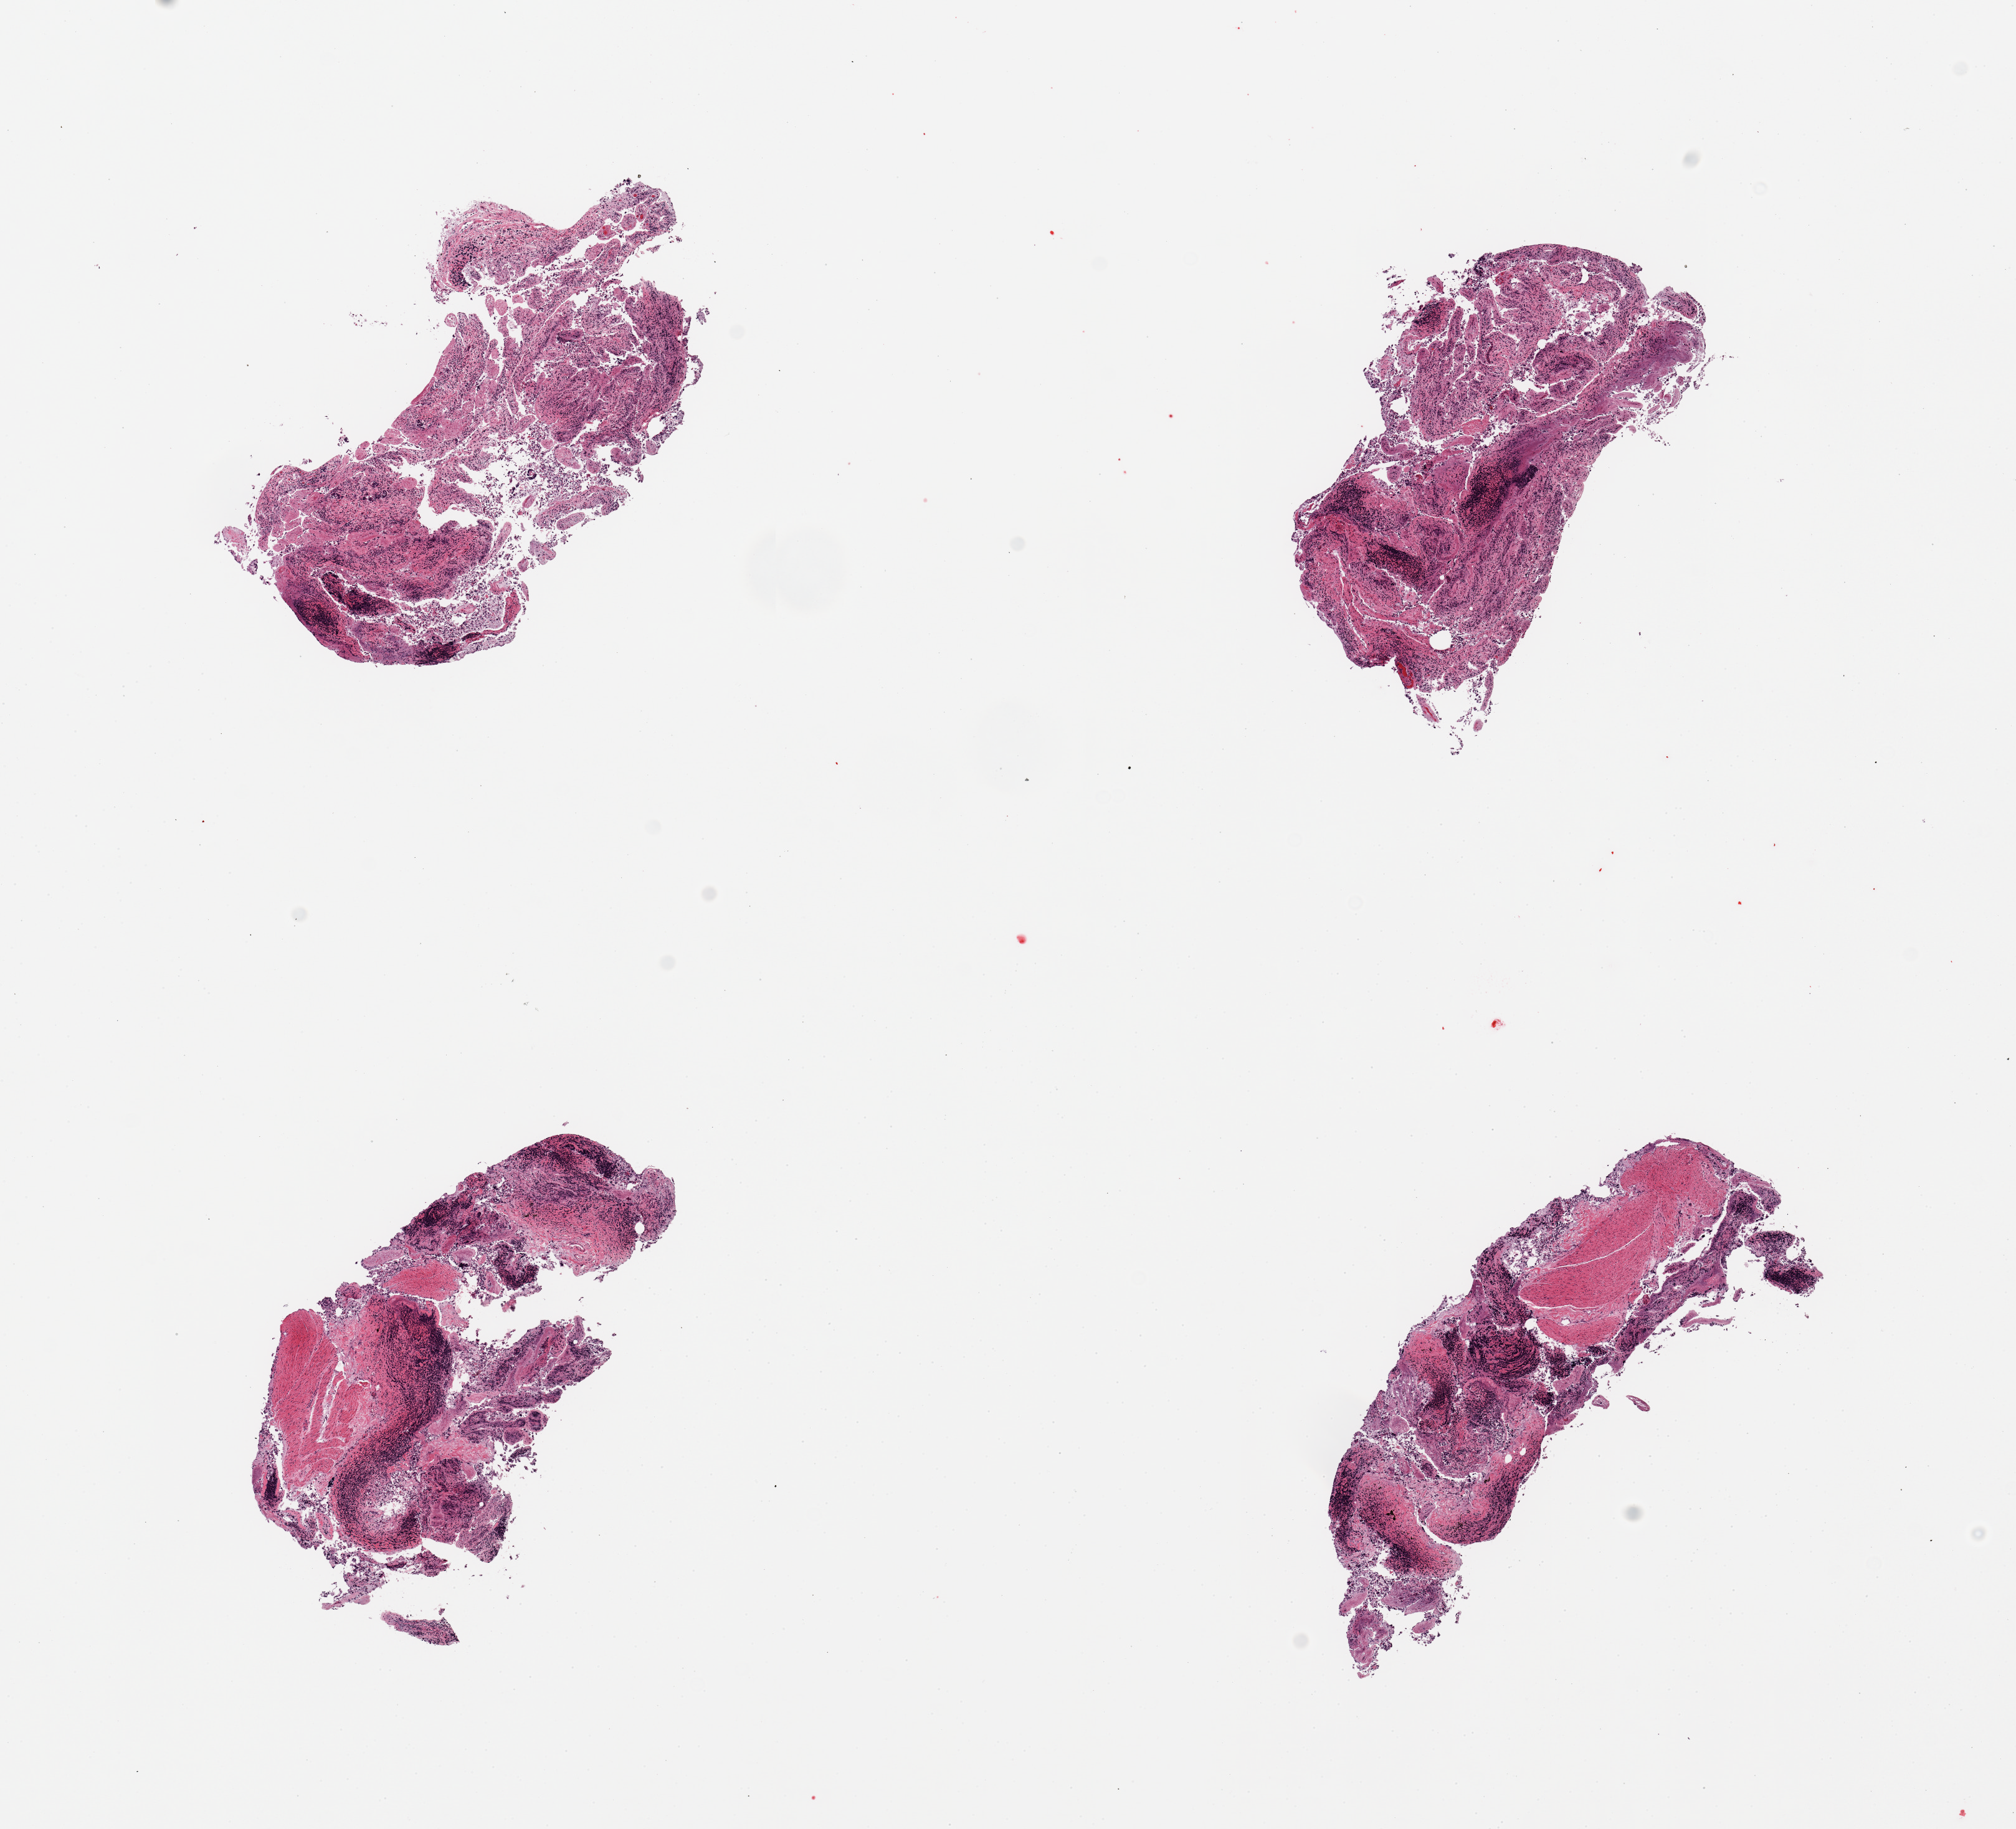
Haematoxylin and eosin whole-slide image — whole scanned area (about 12.8 x 11.6 mm, from a 20x scan) shown as a low-resolution overview, PAXgene-fixed paraffin-embedded (PFPE) section, target tissue: ileum, donor tissue sample. Donor: female.
Review note (as recorded): 4 pieces; lymphoid tissue autolyzed and dispersed; muscle content in 2 oieces.